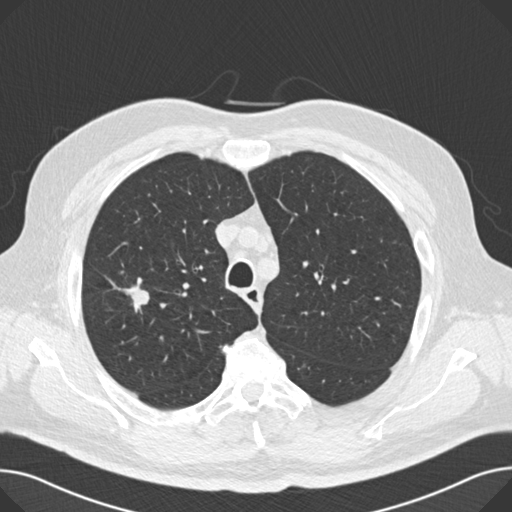
Chest CT (low-dose screening protocol), one axial image; second annual screen; lung window (W 1500 / L -600 HU); standard (soft-tissue) reconstruction kernel (B30f); slice 43 of 166 in the series; 512 × 512 image matrix. Male, age 67 years at enrolment.
Expert reader's lesion annotation, bounding box [x1, y1, x2, y2] px = [123, 281, 155, 312]. No non-calcified nodule or mass ≥4 mm was recorded by the screening reader at this exam. Official screen result: negative screen, significant abnormalities not suspicious for lung cancer.